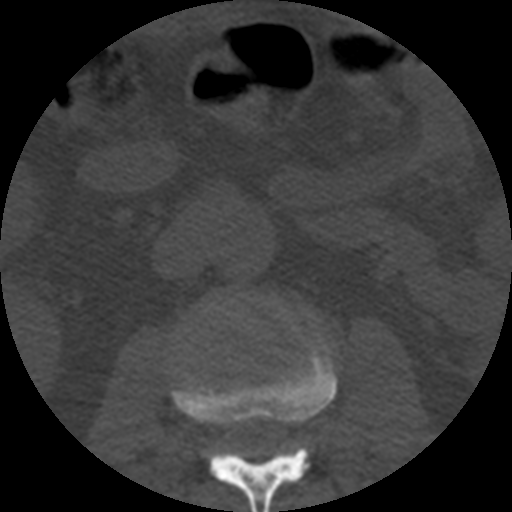
CT including the spine, one axial slice; slice 143 of 508 in the series (ordered by position); reconstruction kernel STANDARD; bone window (W 1800 / L 400 HU); 1.25 mm slice thickness; 512 × 512 image matrix. Patient age 57 years. Case-level facts recorded for this patient, not image findings: primary cancer: prostate.
Structures marked on this image (semi-automatically segmented with operator editing):
- L2 vertebra: bounding box [x1, y1, x2, y2] px = [171, 334, 337, 512]